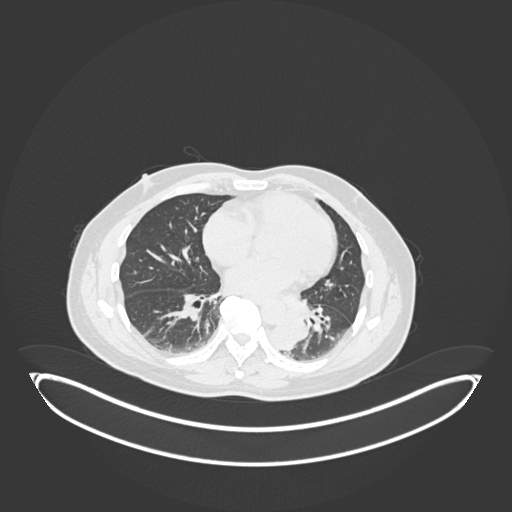
Chest CT, one axial slice. Slice 77 of 258 in the series (ordered by position). Reconstruction kernel B30f. 120 kVp. Lung window (W 1500 / L -600 HU). 512 × 512 image matrix, field of view 500 × 500 mm. Male patient, age 54 years. Case-level facts recorded for this patient, not image findings: clinical TNM (as recorded): T3 N0 M0.
Annotated regions visible in this slice (bounding box drawn by a radiologist):
- lung tumour (recorded histology: squamous cell carcinoma): box from (x=269, y=307) to (x=315, y=358) px